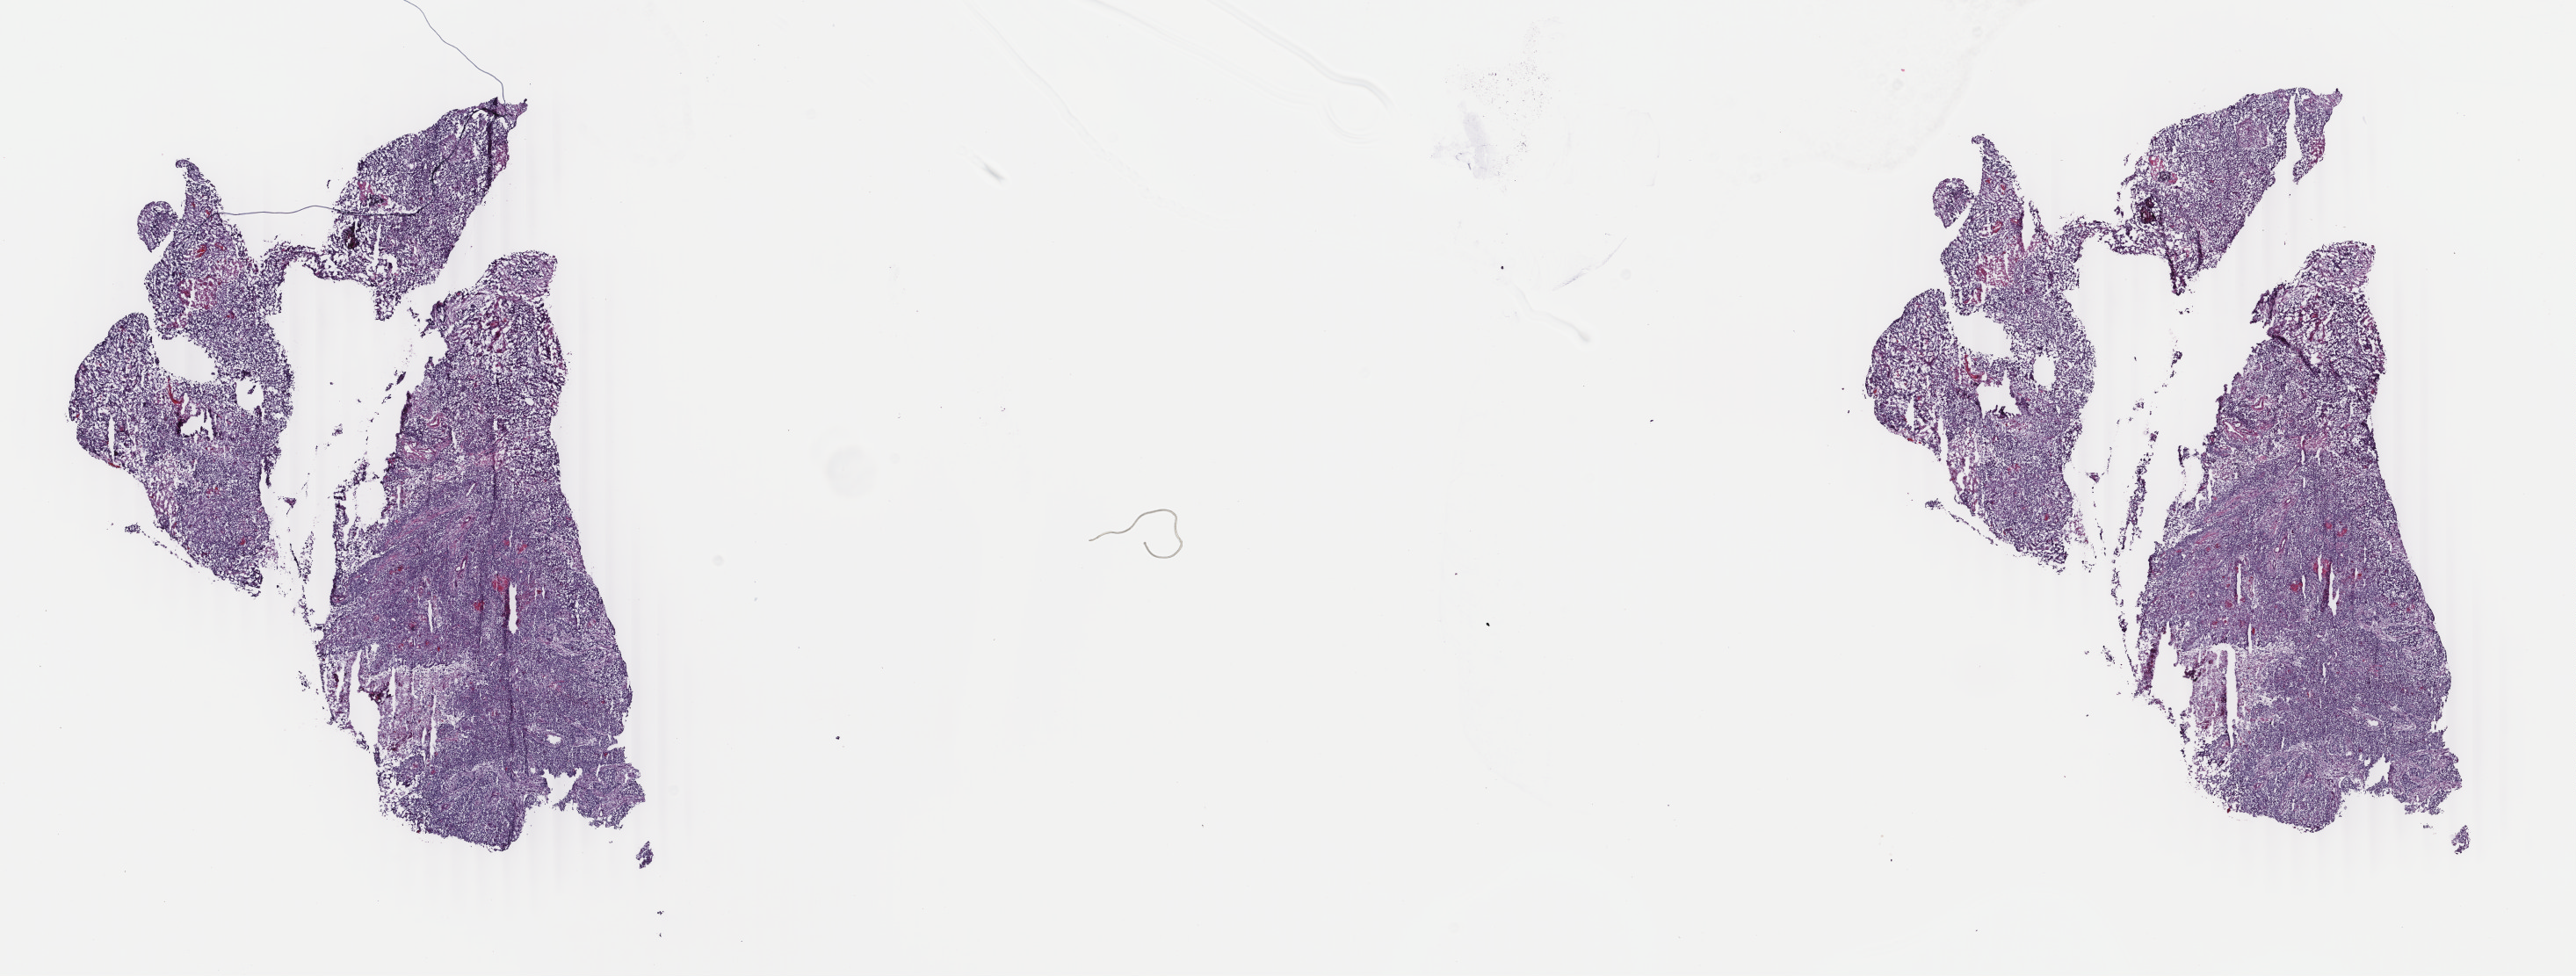
Hematoxylin and eosin (H&E) stained whole-slide image — shown as a low-resolution overview of the whole scanned area (about 23.3 x 8.8 mm, acquisition: 40x scan), frozen section from the top of the tissue portion, primary tumour sample from the uterus. Patient: female, age at initial diagnosis 67 years. Histologic grade: G3 (poorly differentiated). Composition of this section per pathologist review: tumour cells 90%, tumour nuclei 95%, normal cells 0%, stromal cells 5%, necrosis 5%. Inflammatory infiltration, as recorded: lymphocyte infiltration 0%, monocyte infiltration 0%, neutrophil infiltration 0%.
FIGO stage: IB. Pathologic diagnosis: Endometrioid adenocarcinoma, NOS (endometrium).